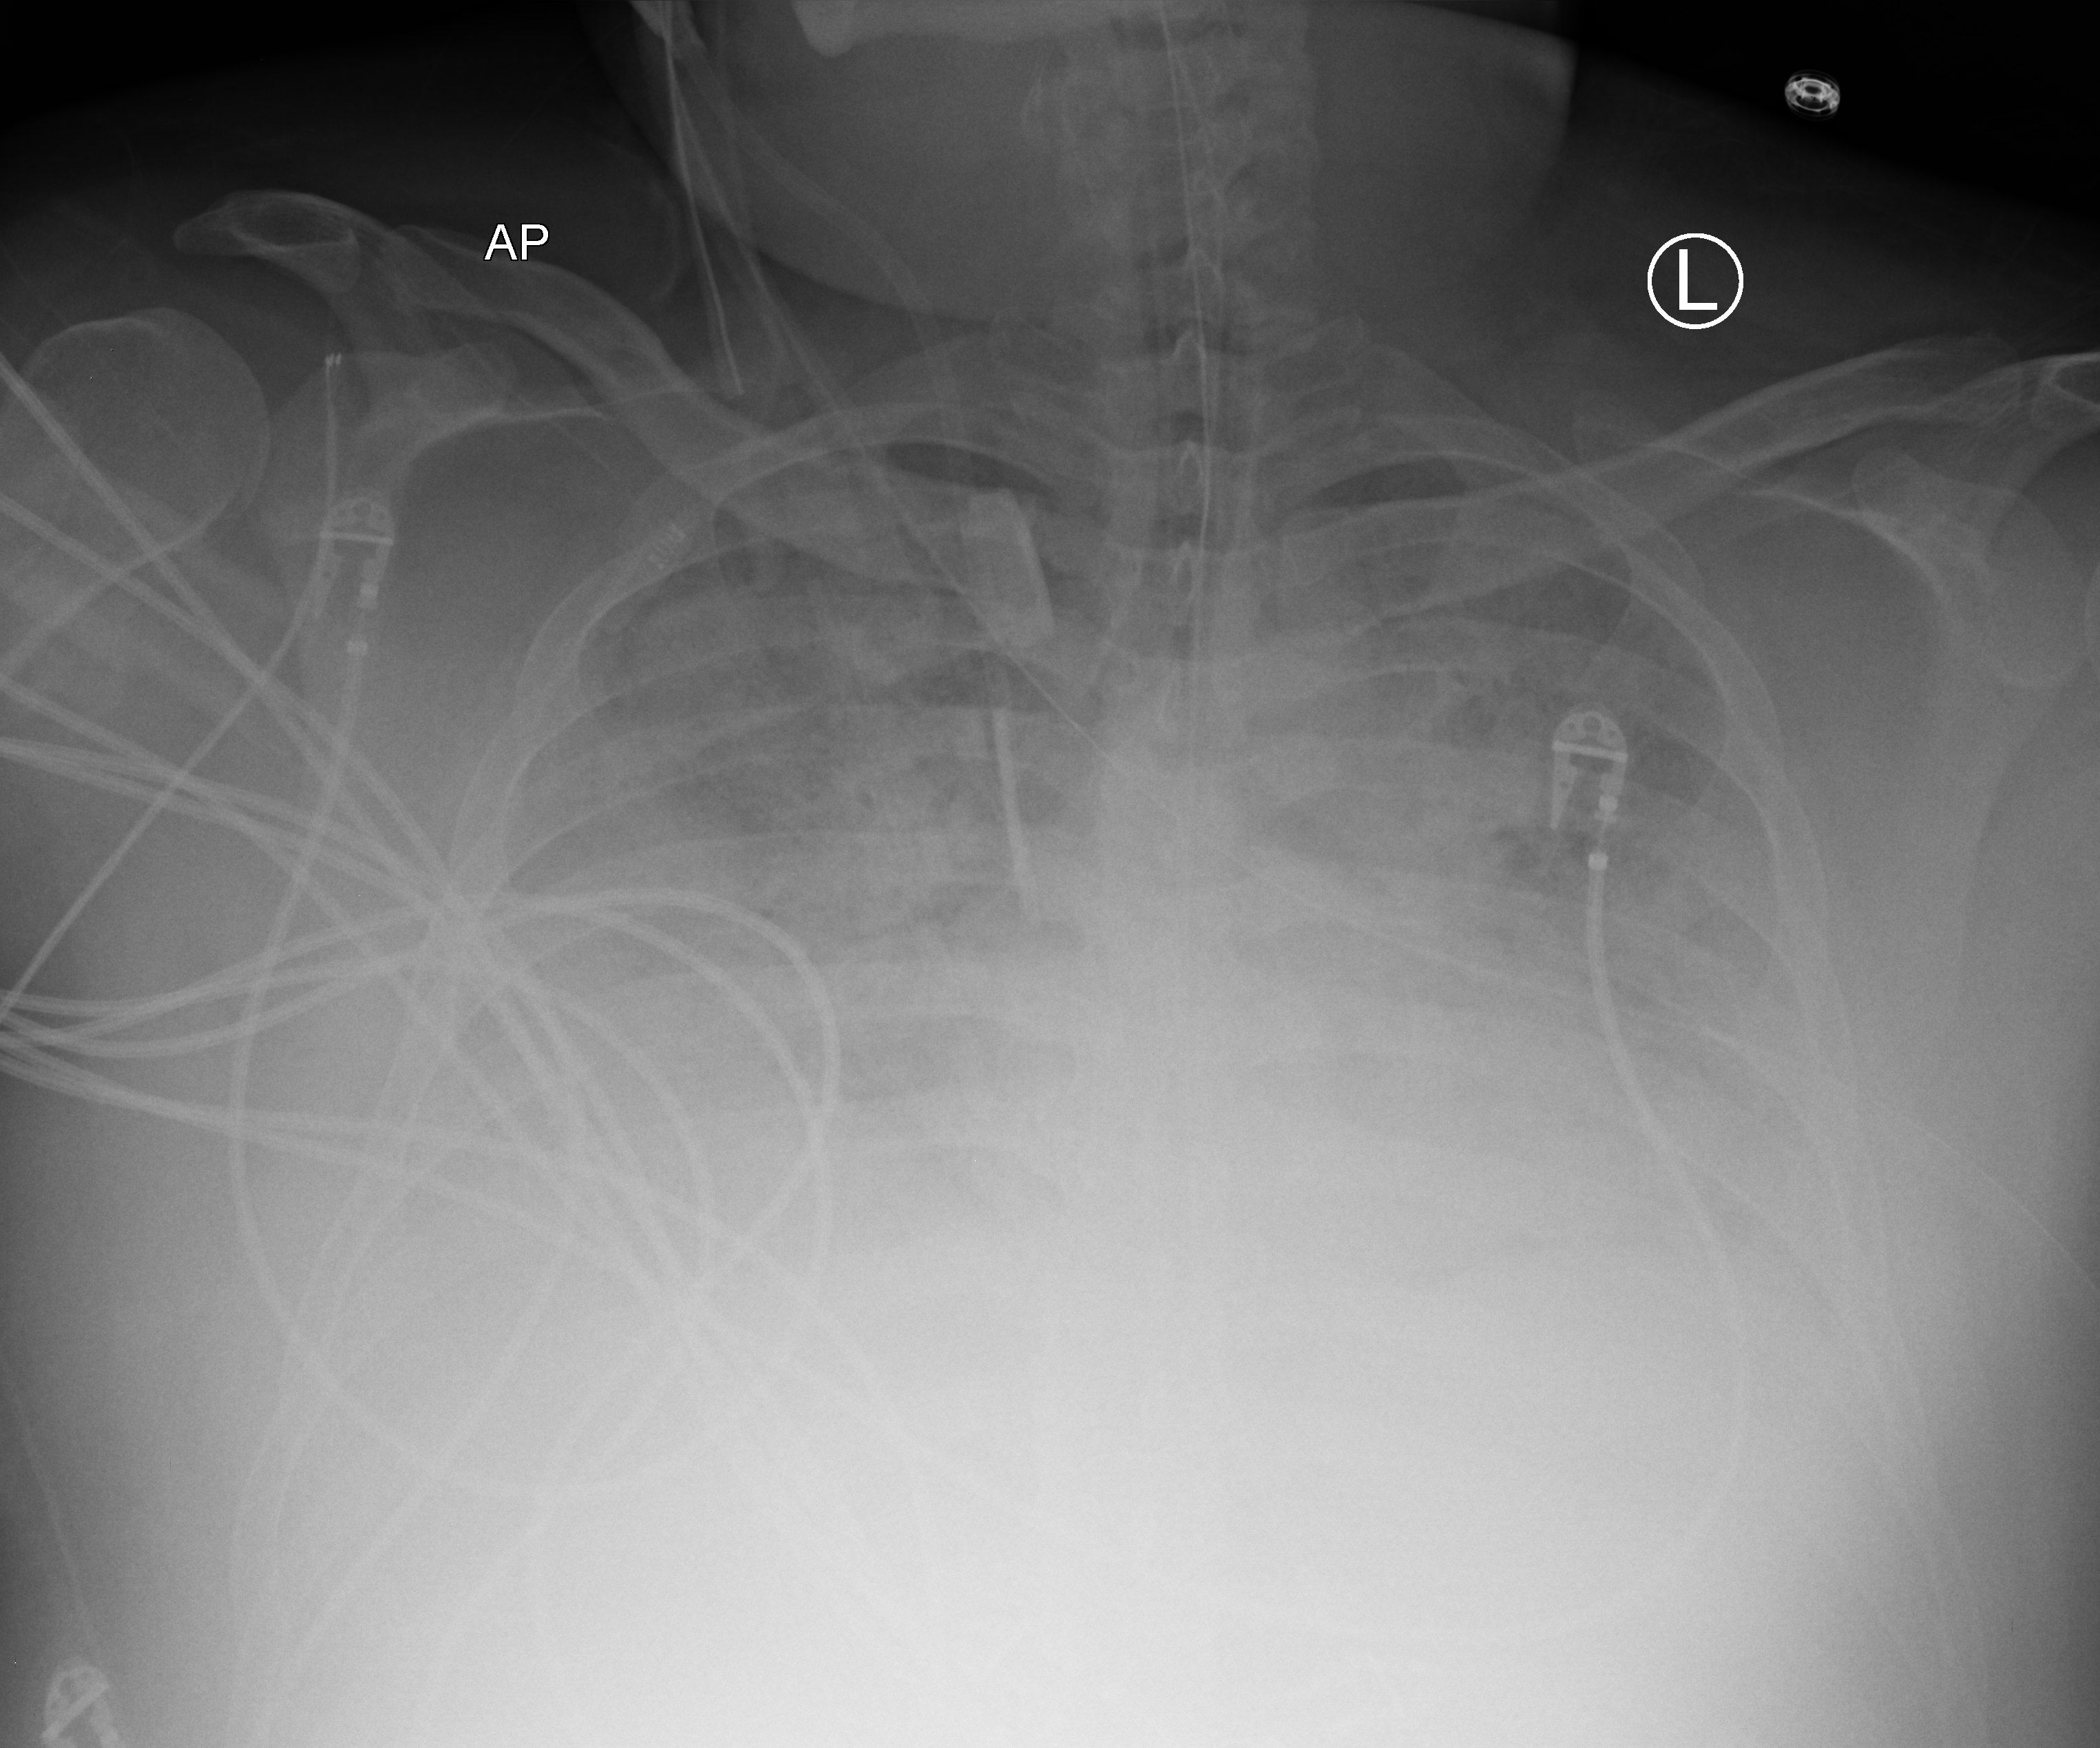
Portable chest radiograph. Patient hospitalised with COVID-19, aged 18–59 years.
Admission-level facts for this patient (not findings on this image; timing relative to this image not recorded): other chronic lung disease (admission record): yes; diabetes (admission record): no; mechanically ventilated during this hospital stay: yes.